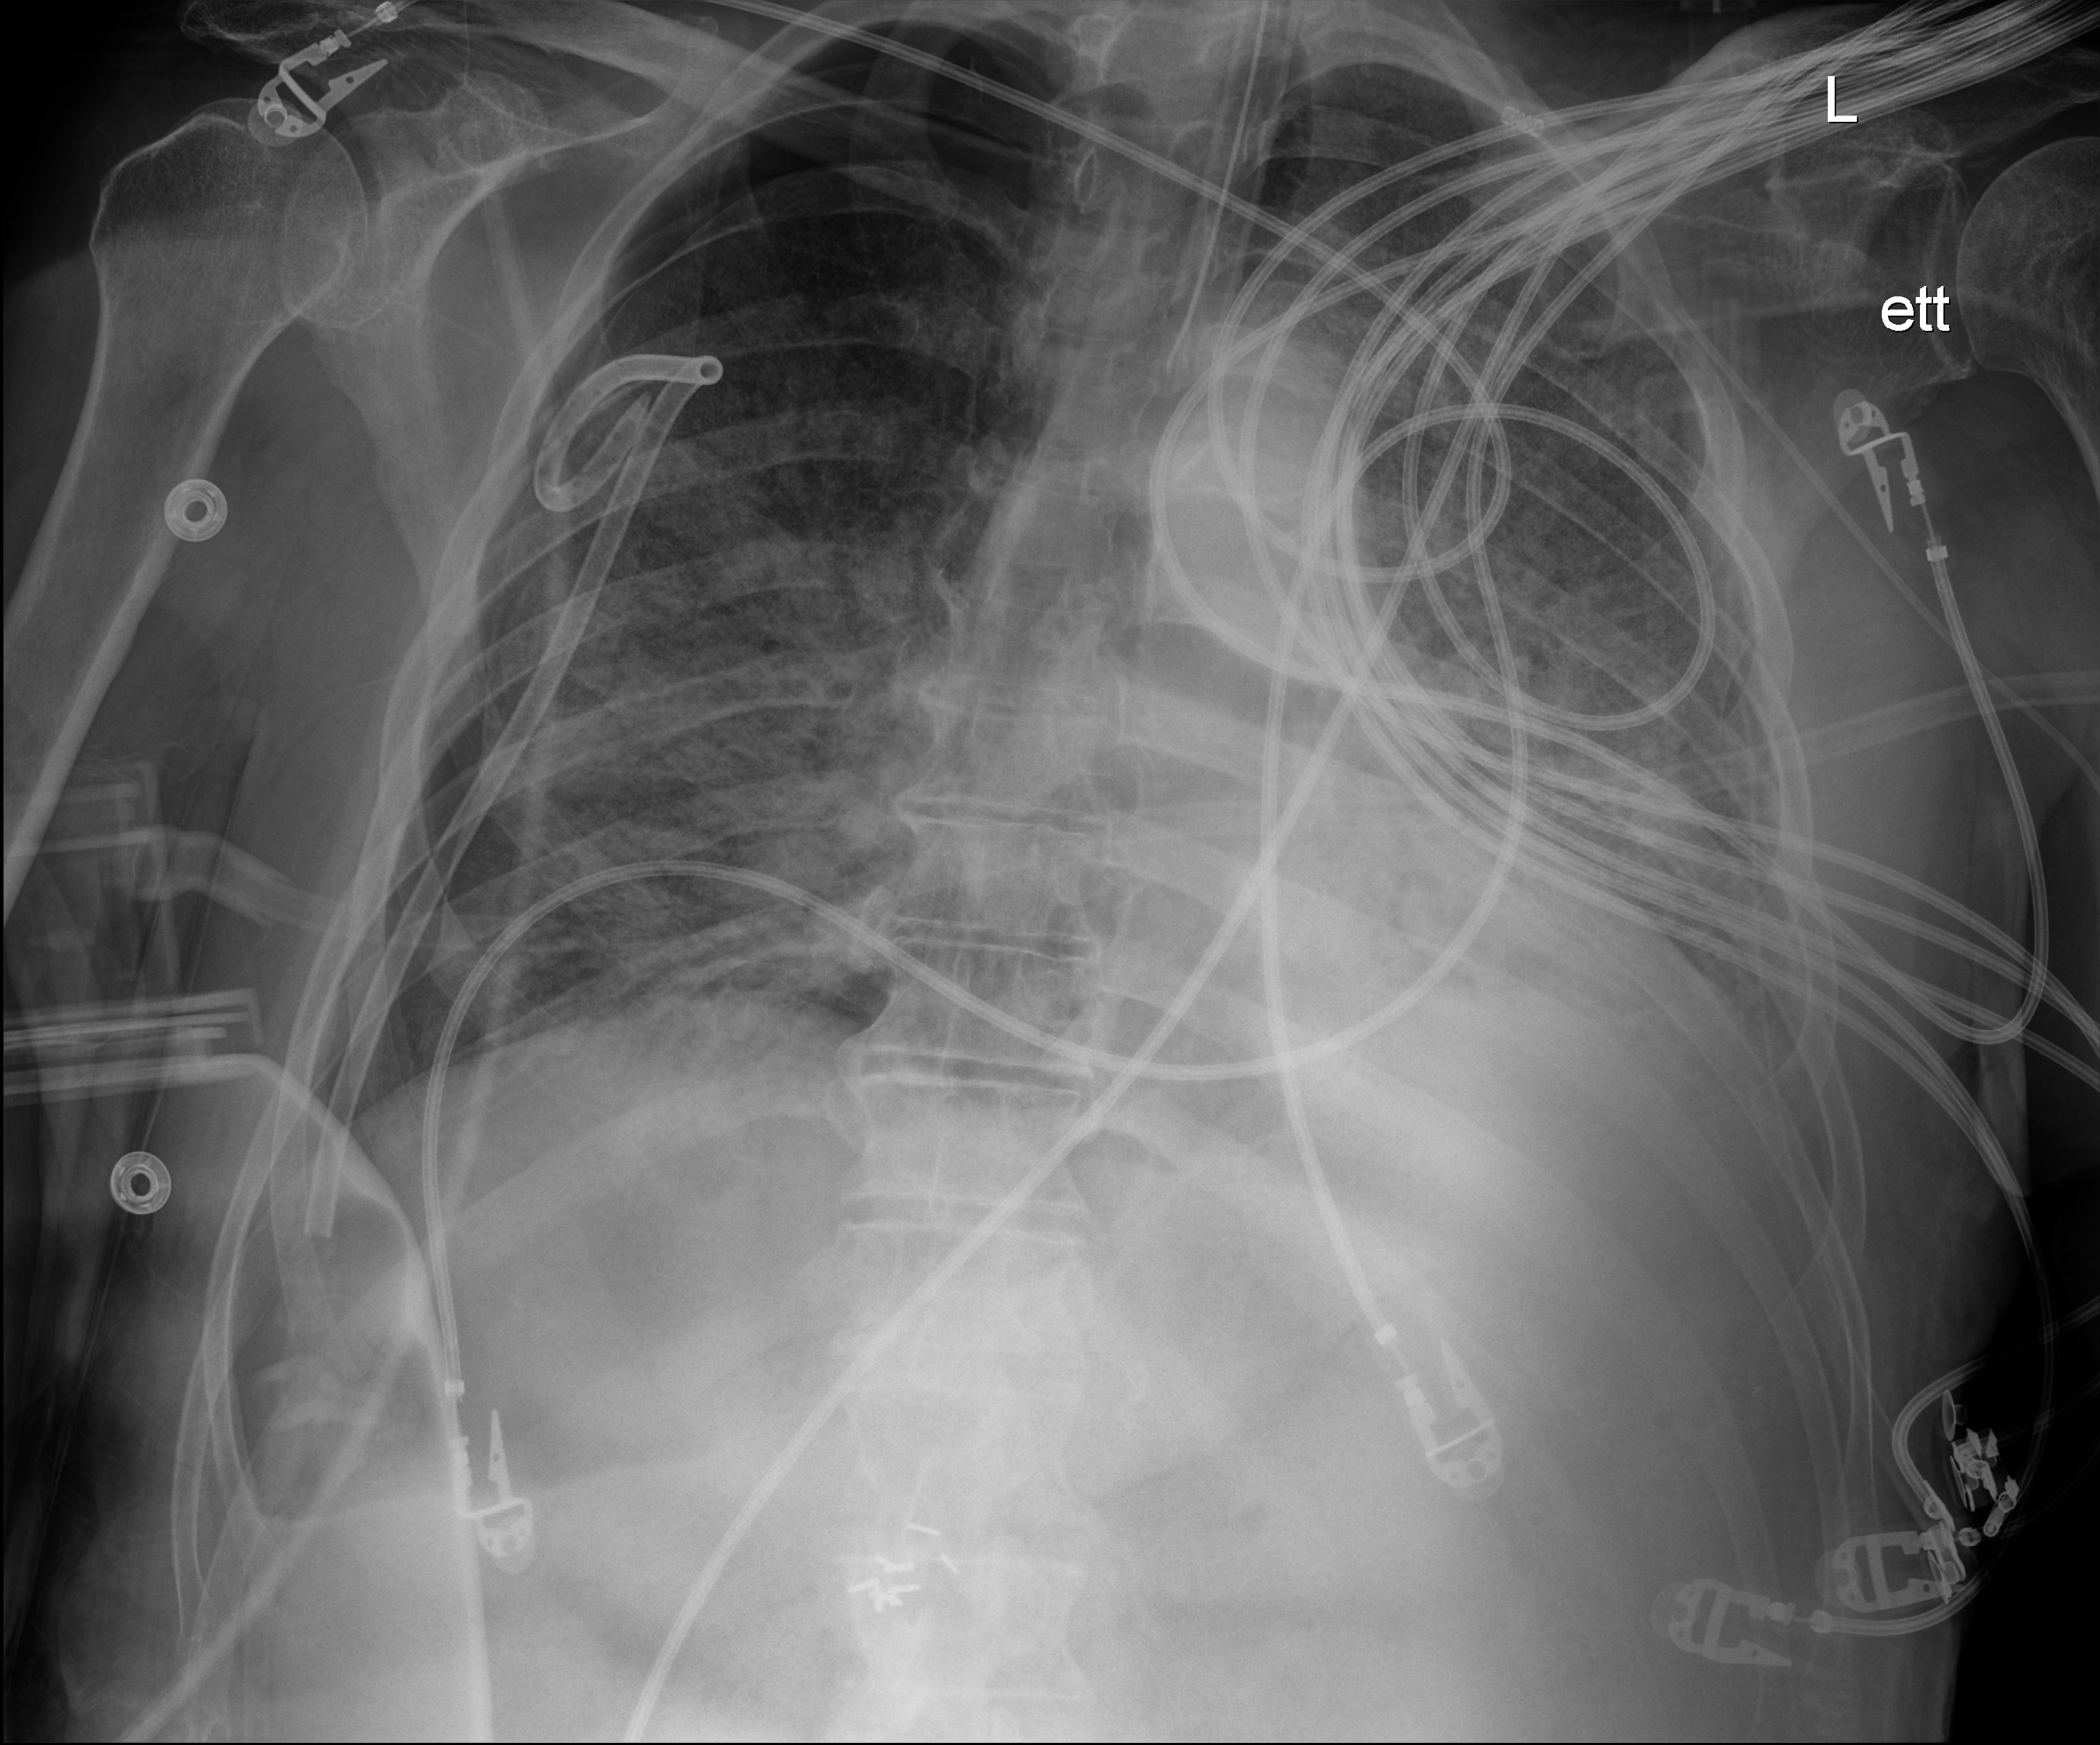
Portable chest radiograph; anteroposterior (AP) projection. Patient hospitalised with COVID-19; male, aged 75–90 years.
Hospital-stay facts (about this admission, not read from this image; timing relative to this image not recorded): mechanically ventilated during this hospital stay: yes; admitted to intensive care during this hospital stay: yes.